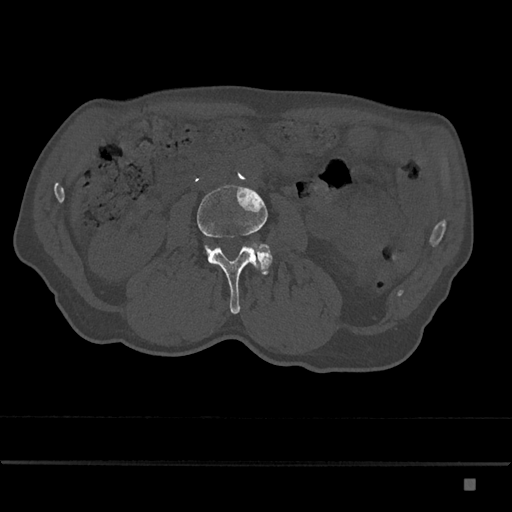
CT including the spine, one axial slice. Position 398 of 797 along the scan axis. Reconstruction kernel Br40s/3. Bone window (W 1800 / L 400 HU). 0.5 mm slice thickness. 512 × 512 image matrix. Patient: male, 72 years. From the clinical record (not read from this slice): primary cancer: prostate.
Structures marked on this image (semi-automatically segmented with operator editing):
- L3 vertebra: bounding box (x1, y1, x2, y2) in pixels: (197, 185, 270, 314)
- L4 vertebra: (251, 244, 273, 275)